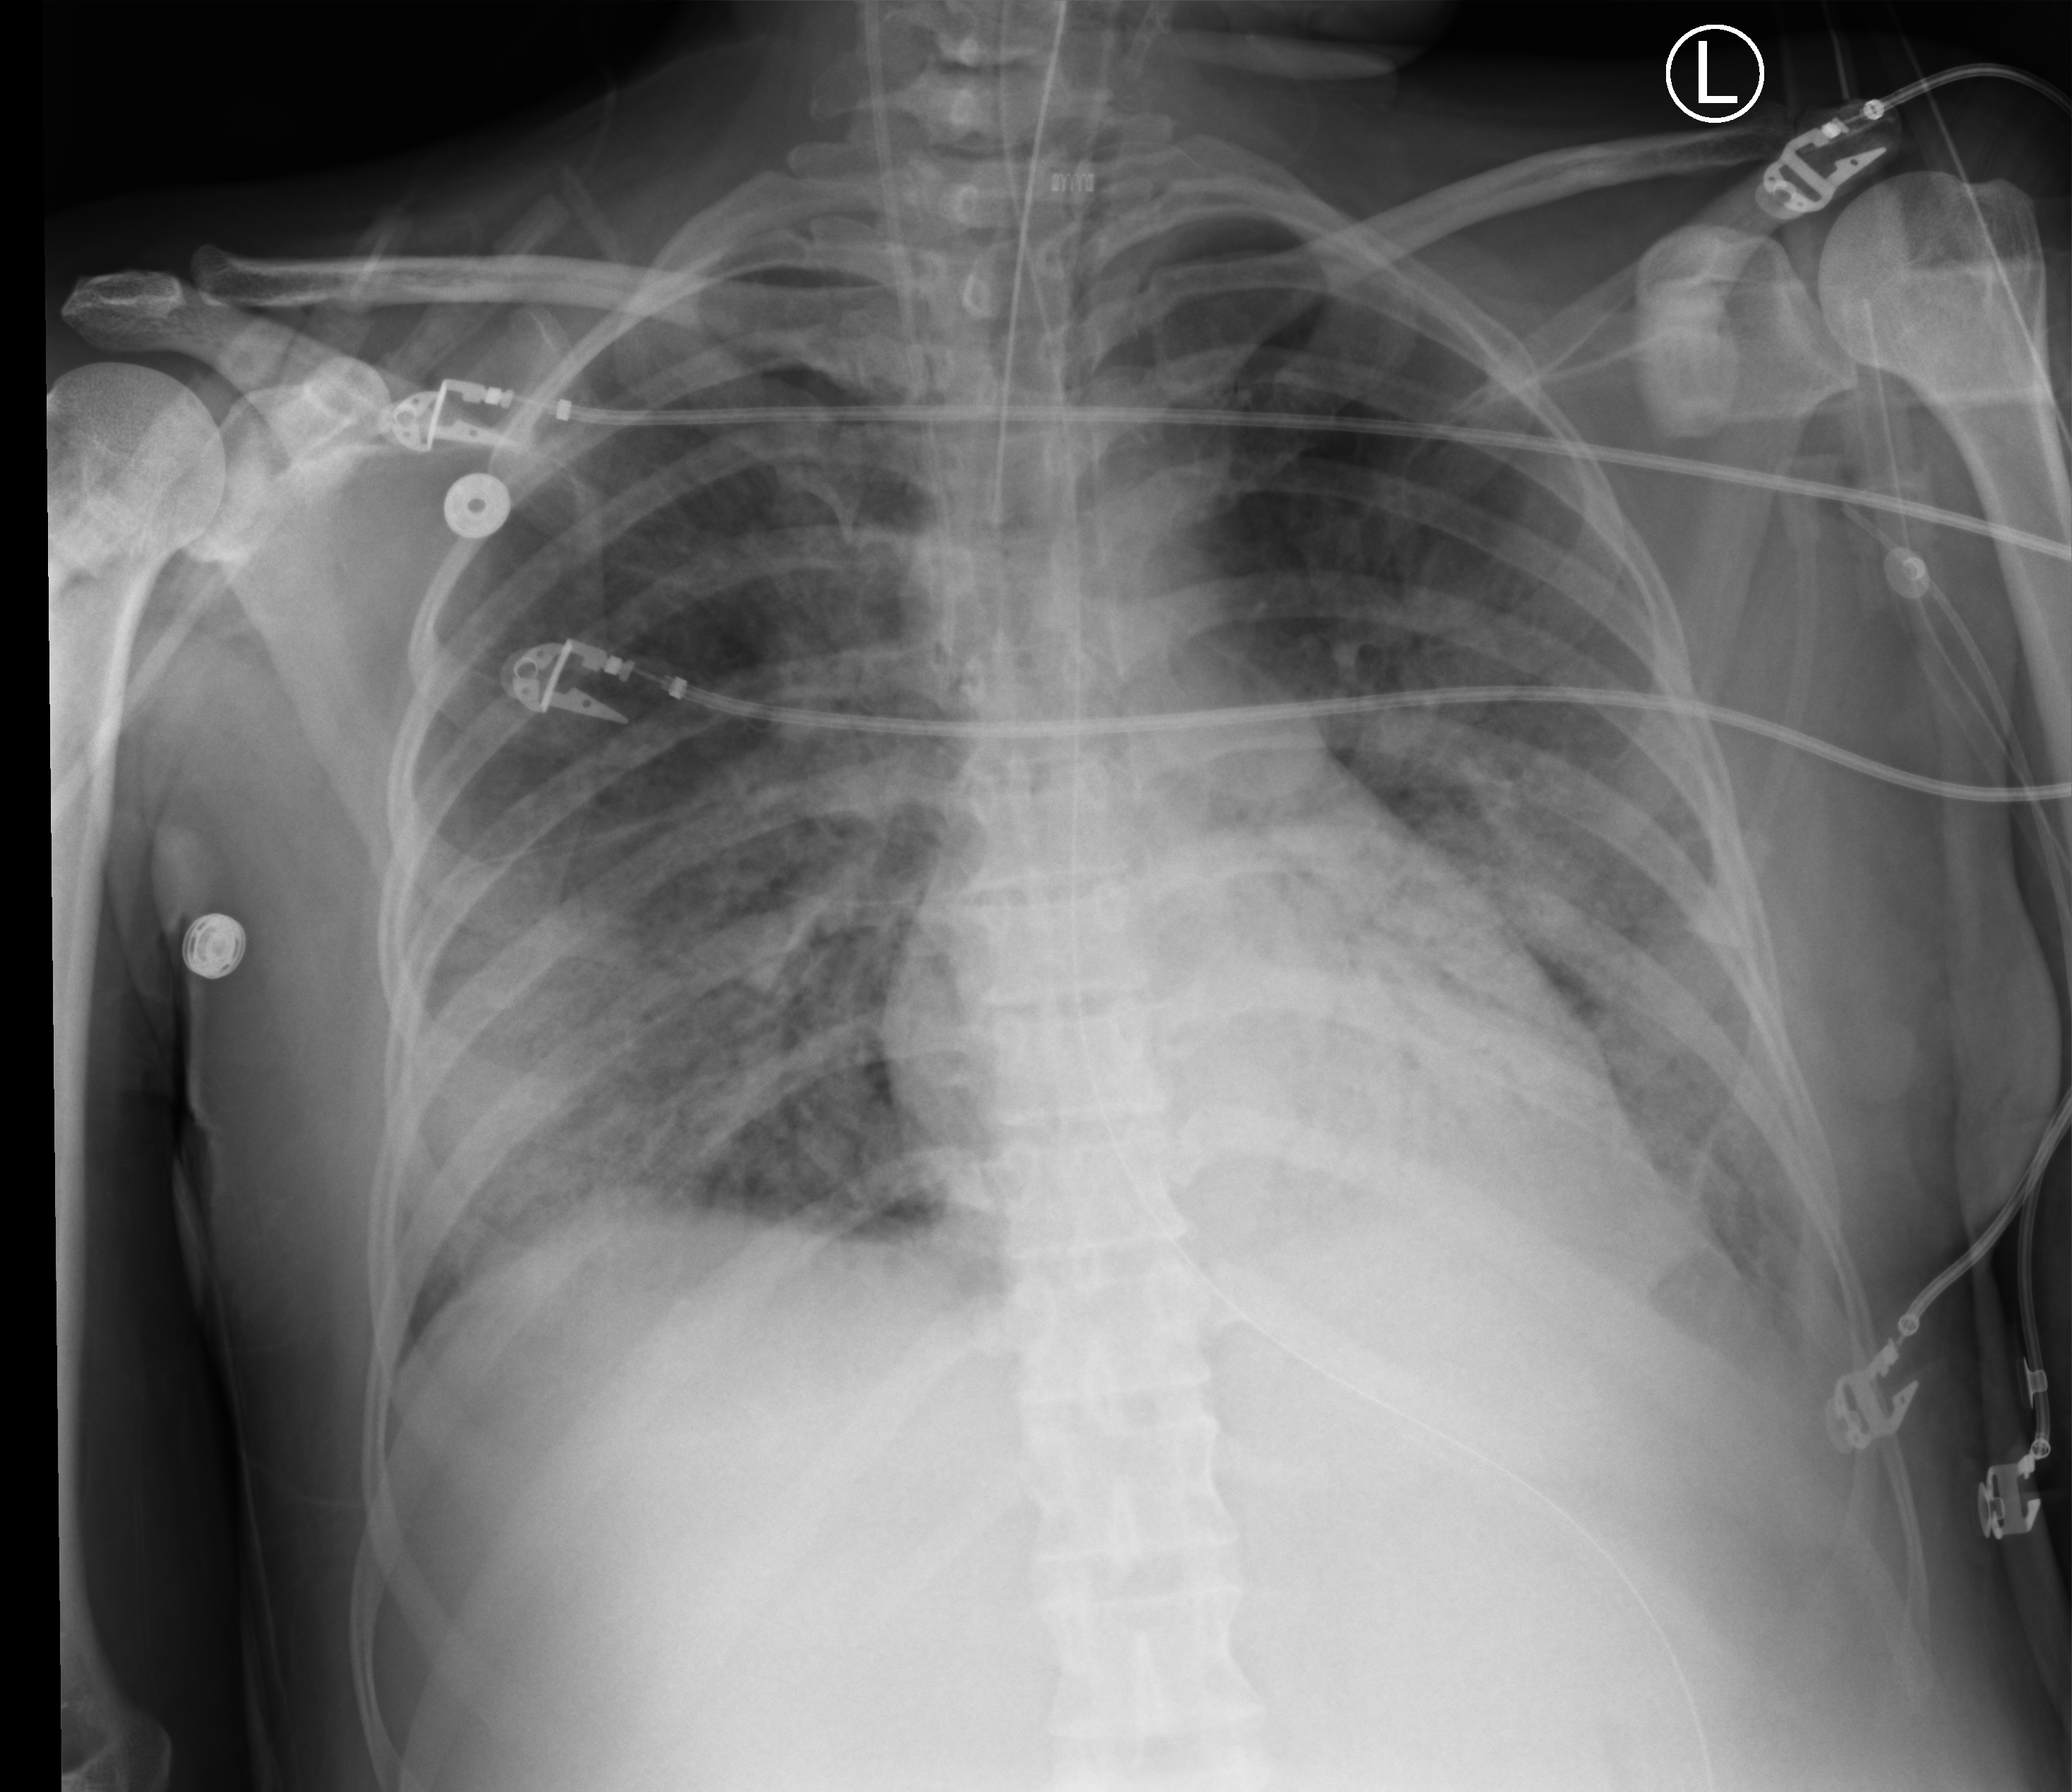
Bedside chest radiograph (computed radiography), anteroposterior (AP) projection. Patient hospitalised with COVID-19; female, aged 18–59 years.
Admission-level facts for this patient (not findings on this image; timing relative to this image not recorded): other chronic lung disease (admission record): no; length of hospital stay: 71 days.